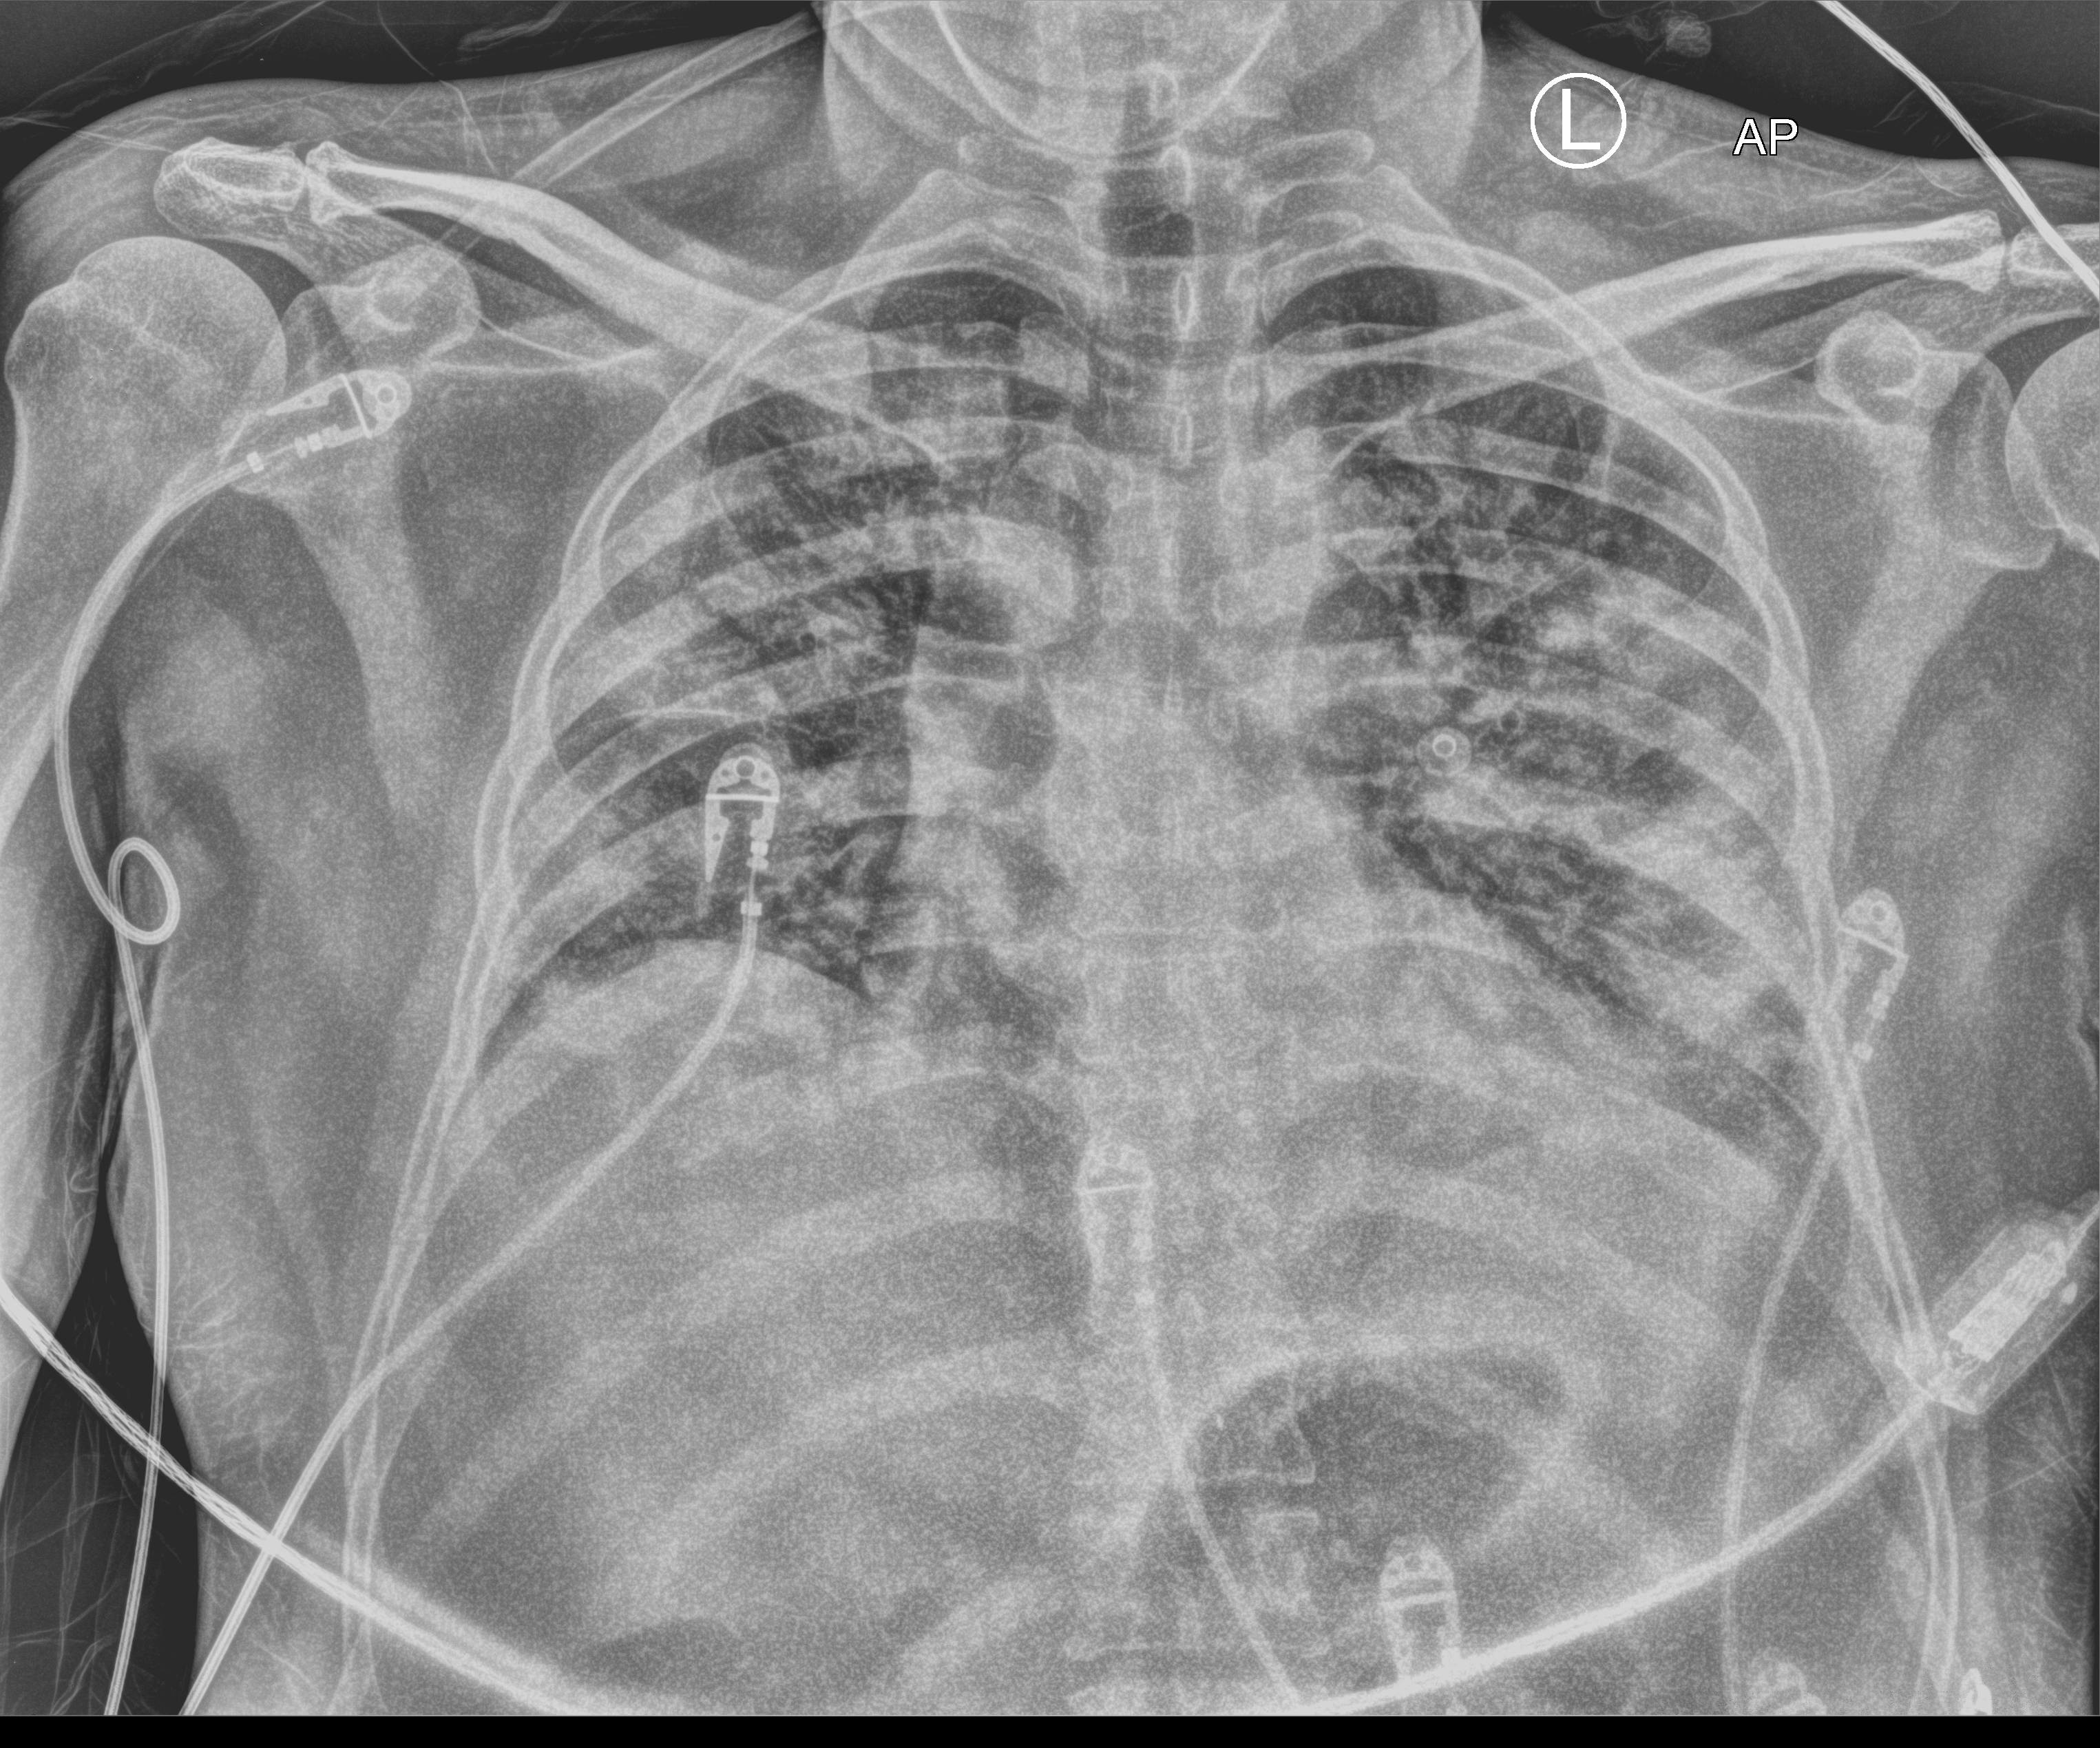
Chest X-ray (portable), anteroposterior (AP) projection. Male patient hospitalised with COVID-19, age 18–59 years.
Hospital-stay facts (about this admission, not read from this image; timing relative to this image not recorded): length of hospital stay: 16 days.